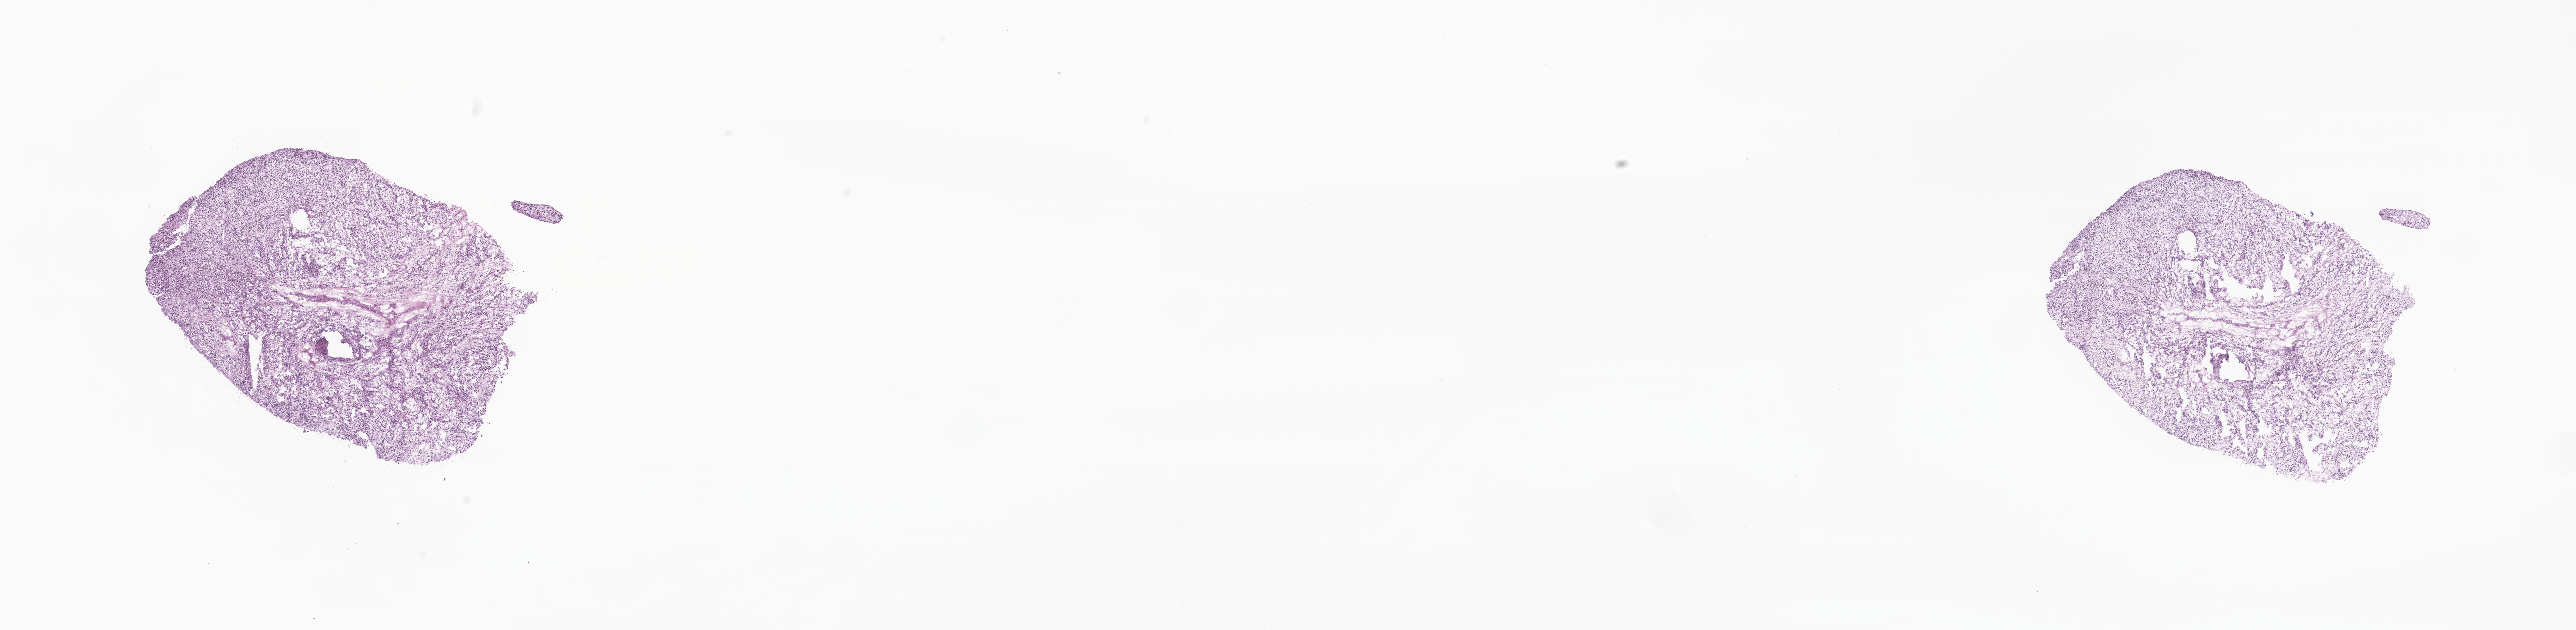
Whole-slide image, H&E stain of tumor tissue from the orbit — shown as a low-resolution overview of the whole scanned area (about 32.4 x 7.9 mm), frozen section. Male patient, age 113 months (9 years 5 months).
* diagnosis (ICD-O-3 morphology term): Embryonal rhabdomyosarcoma, NOS